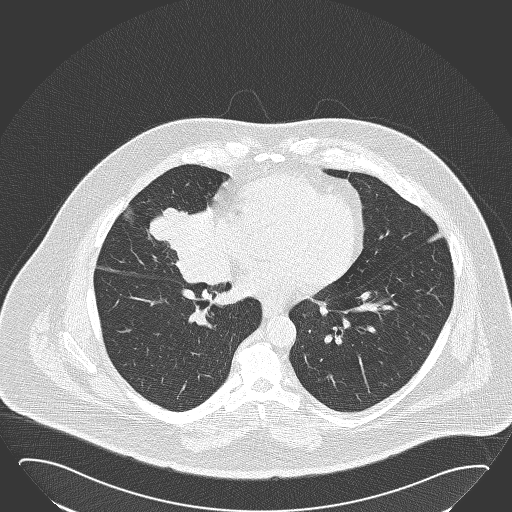
Axial slice from a low-dose chest CT screening exam; first (baseline) screen; lung window (W 1500 / L -600 HU); 2 mm slice thickness; 120 kVp; slice 96 of 168 in the series; 512 × 512 image matrix. Male participant, aged 61 years at enrolment.
Expert reader's lesion annotation, bounding box (x1, y1, x2, y2) in pixels: (141, 189, 230, 276). The screening reader recorded 2 non-calcified nodules or masses ≥4 mm on this exam (right middle lobe, left lower lobe); which of them this box marks is not recorded. Later outcome: lung cancer diagnosed 47 days after this screen — basaloid squamous cell carcinoma, right middle lobe, right hilum, poorly differentiated (G3), stage IIB (AJCC 6th edition), 95 mm at pathology.